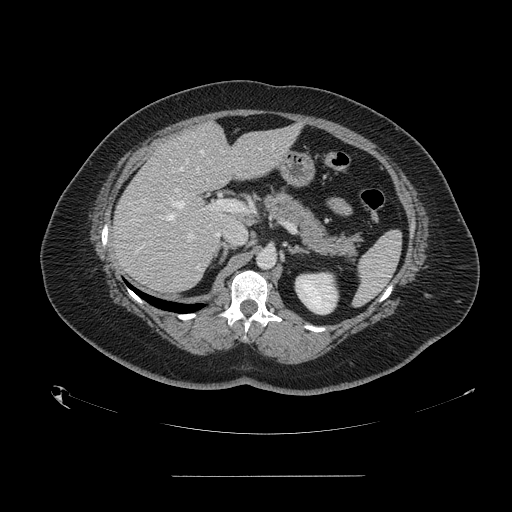
Contrast-enhanced abdominal CT, one axial slice. Position 90 of 164 along the scan axis. Soft-tissue window (W 400 / L 40 HU). 2.5 mm slice thickness. 512 × 512 image matrix, field of view 495 × 495 mm. Female patient, age 52 years. Case-level facts recorded for this patient, not image findings: diagnosis: colorectal cancer liver metastases, imaged before liver resection; multiple liver metastases: yes; largest metastasis: 3.5 cm; chemotherapy before resection: no.
Outlined on this slice (expert manual segmentation):
- hepatic veins: box from (x=166, y=145) to (x=273, y=220) px
- liver: (x=113, y=124)–(x=297, y=292)
- planned liver remnant (the part of the liver to remain after resection): (x=177, y=124)–(x=297, y=225)
- portal vein (with intrahepatic branches): (x=175, y=189)–(x=245, y=238)